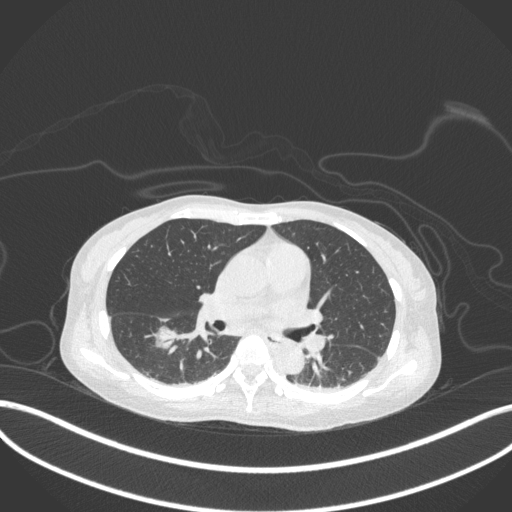
Chest CT, one axial slice. Slice 169 of 260 in the series (ordered by position). Reconstruction kernel B31f. 120 kVp. Lung window (W 1500 / L -600 HU). 1 mm slice thickness. 512 × 512 image matrix, field of view 400 × 400 mm. Female patient, age 44 years. Case-level facts recorded for this patient, not image findings: clinical TNM (as recorded): T1c N0 M0.
Outlined on this slice (bounding box drawn by a radiologist):
- lung tumour (recorded histology: adenocarcinoma): bounding box (x1, y1, x2, y2) in pixels: (148, 321, 178, 351)